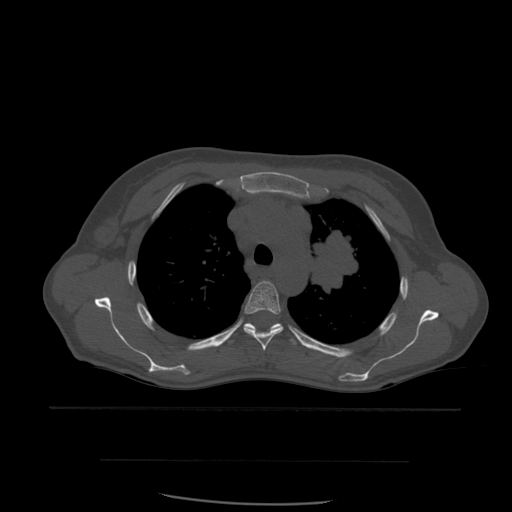
CT including the spine, one axial slice; position 423 of 574 along the scan axis; bone window (W 1800 / L 400 HU); 512 × 512 image matrix. Patient age 48 years. Case-level facts recorded for this patient, not image findings: primary cancer: lung; vertebrae with lytic lesions (as recorded): T11.
Outlined on this slice (semi-automatically segmented with operator editing):
- T4 vertebra: box from (x=244, y=281) to (x=284, y=351) px
- T5 vertebra: (x=228, y=323)–(x=302, y=346)